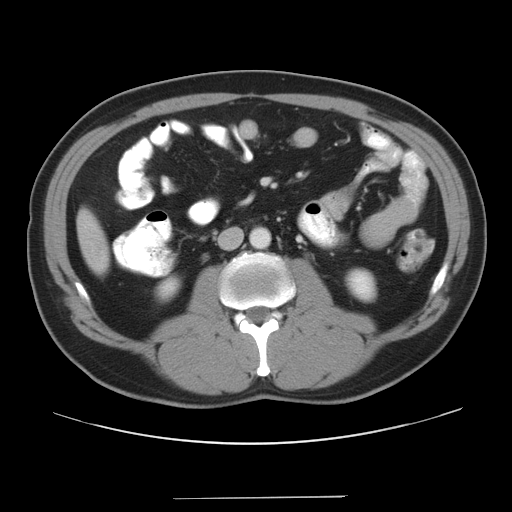
Contrast-enhanced abdominal CT, one axial slice. Slice 11 of 37 in the series (ordered by position). 120 kVp. Intravenous contrast given. Soft-tissue window (W 400 / L 40 HU). 7.5 mm slice thickness. 512 × 512 image matrix. Male patient, age 46 years. Case-level facts recorded for this patient, not image findings: diagnosis: colorectal cancer liver metastases, imaged before liver resection; multiple liver metastases: yes; largest metastasis: 1 cm.
Structures marked on this image (manually delineated by an expert):
- liver: bounding box [x1, y1, x2, y2] px = [79, 215, 107, 271]
- planned liver remnant (the part of the liver to remain after resection): [79, 214, 107, 272]